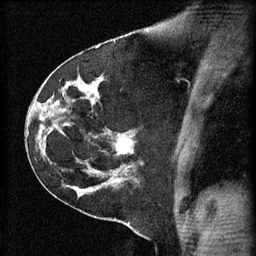
Breast MRI (dynamic contrast-enhanced), one sagittal slice; position 37 of 60 along the scan axis; 3 images stored at this slice position (order not interpretable as contrast timing); 1.5 T; TE 4.2 ms, TR 11 ms; 2 mm slice thickness; 256 × 256 image matrix, field of view 180 × 180 mm. Female patient, age 45 years.
Outlined on this slice (semi-automatically segmented with operator editing):
- analysis volume of interest (the breast-tissue region the enhancement analysis was run in; not a lesion): bounding box <106,132,143,171> (left, top, right, bottom; pixels)
- tumour enhancement mask (voxels above the 70 % enhancement threshold inside the analysis volume of interest): <116,138,133,155>